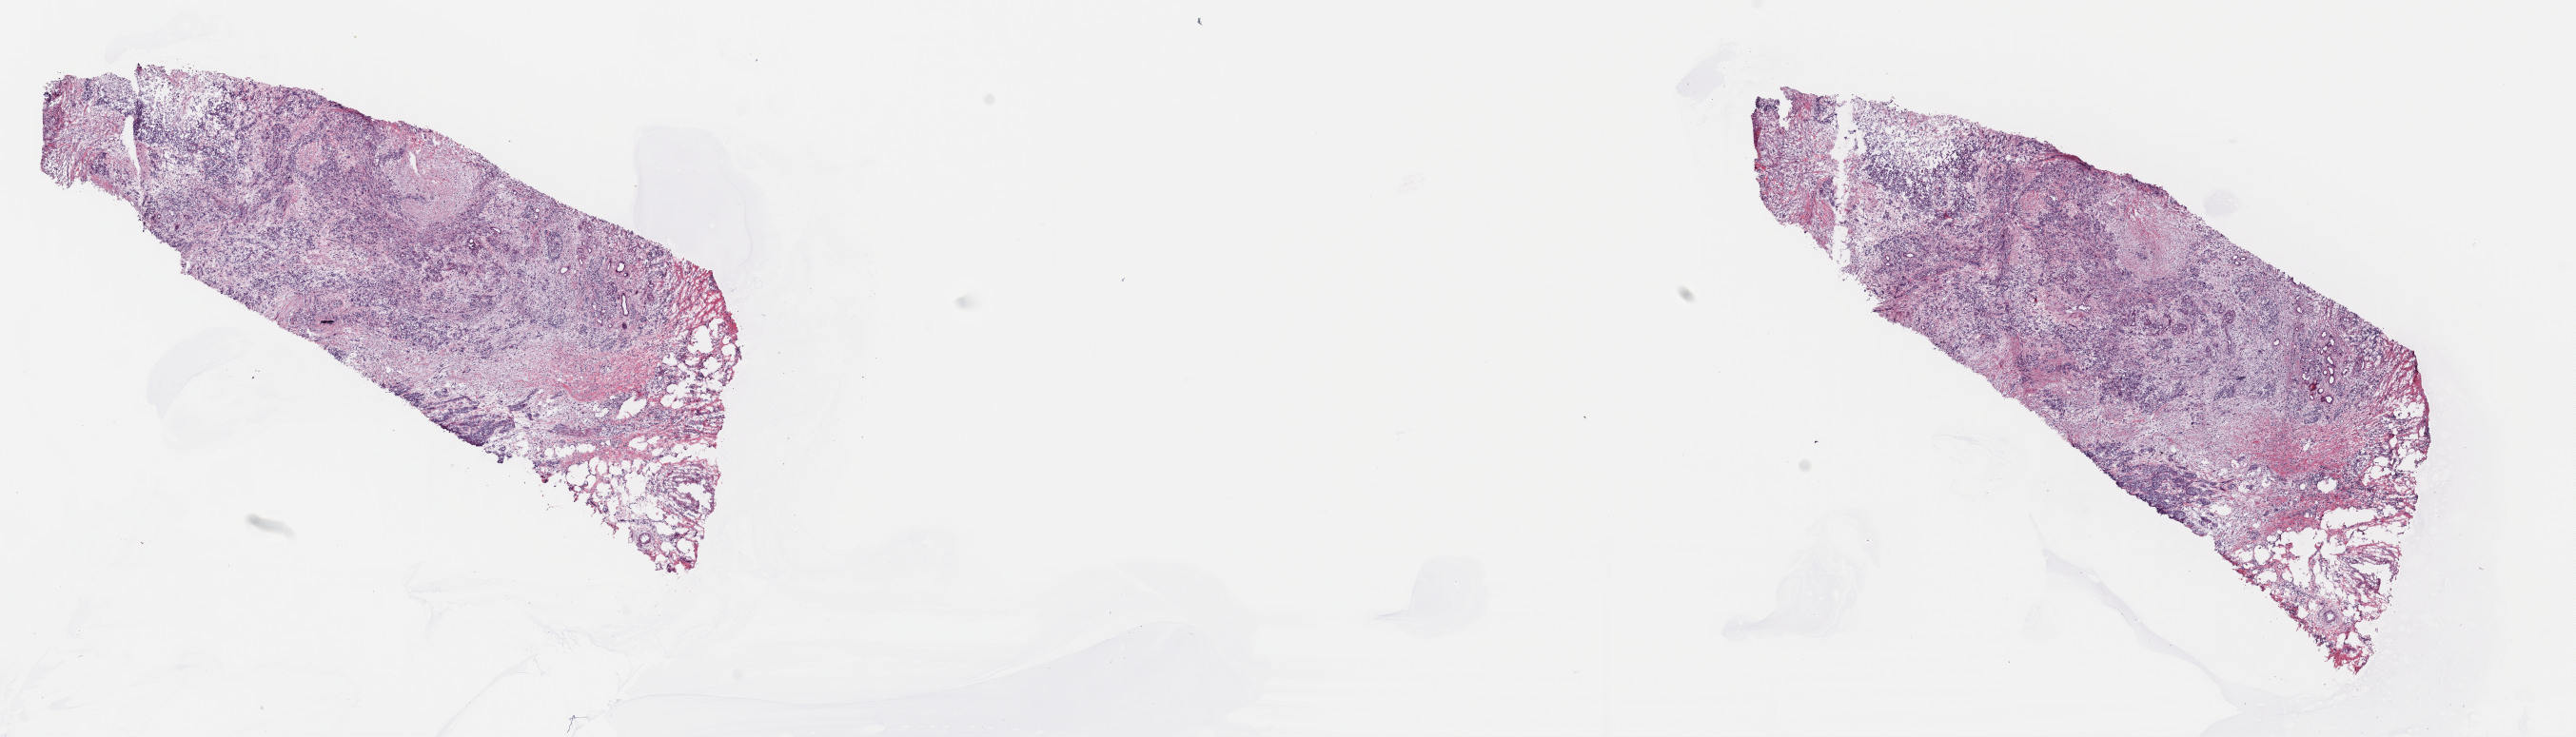
H&E-stained whole-slide image — low-resolution overview of the scanned area, about 21.3 x 6.1 mm, frozen section from the top of the tissue portion, pancreas, primary tumour sample. Male patient; age at initial diagnosis 74 years. Composition of this section per pathologist review: tumour cells 95%, tumour nuclei 65%.
Histologic diagnosis: Infiltrating duct carcinoma, NOS (head of pancreas).